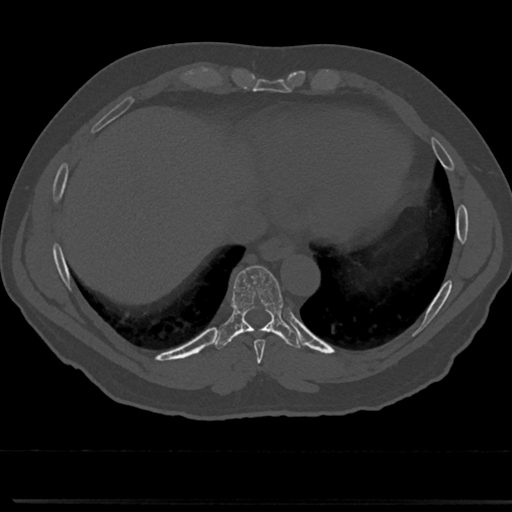
CT including the spine, one axial slice; slice 317 of 817 in the series (ordered by position); reconstruction kernel Br40s/3; bone window (W 1800 / L 400 HU); 512 × 512 image matrix. Male patient, age 61 years. From the clinical record (not read from this slice): primary cancer: prostate.
Outlined on this slice (semi-automatic segmentation, software-assisted and operator-edited):
- T7 vertebra: bounding box <258,364,265,375> (left, top, right, bottom; pixels)
- T8 vertebra: <219,267,304,355>